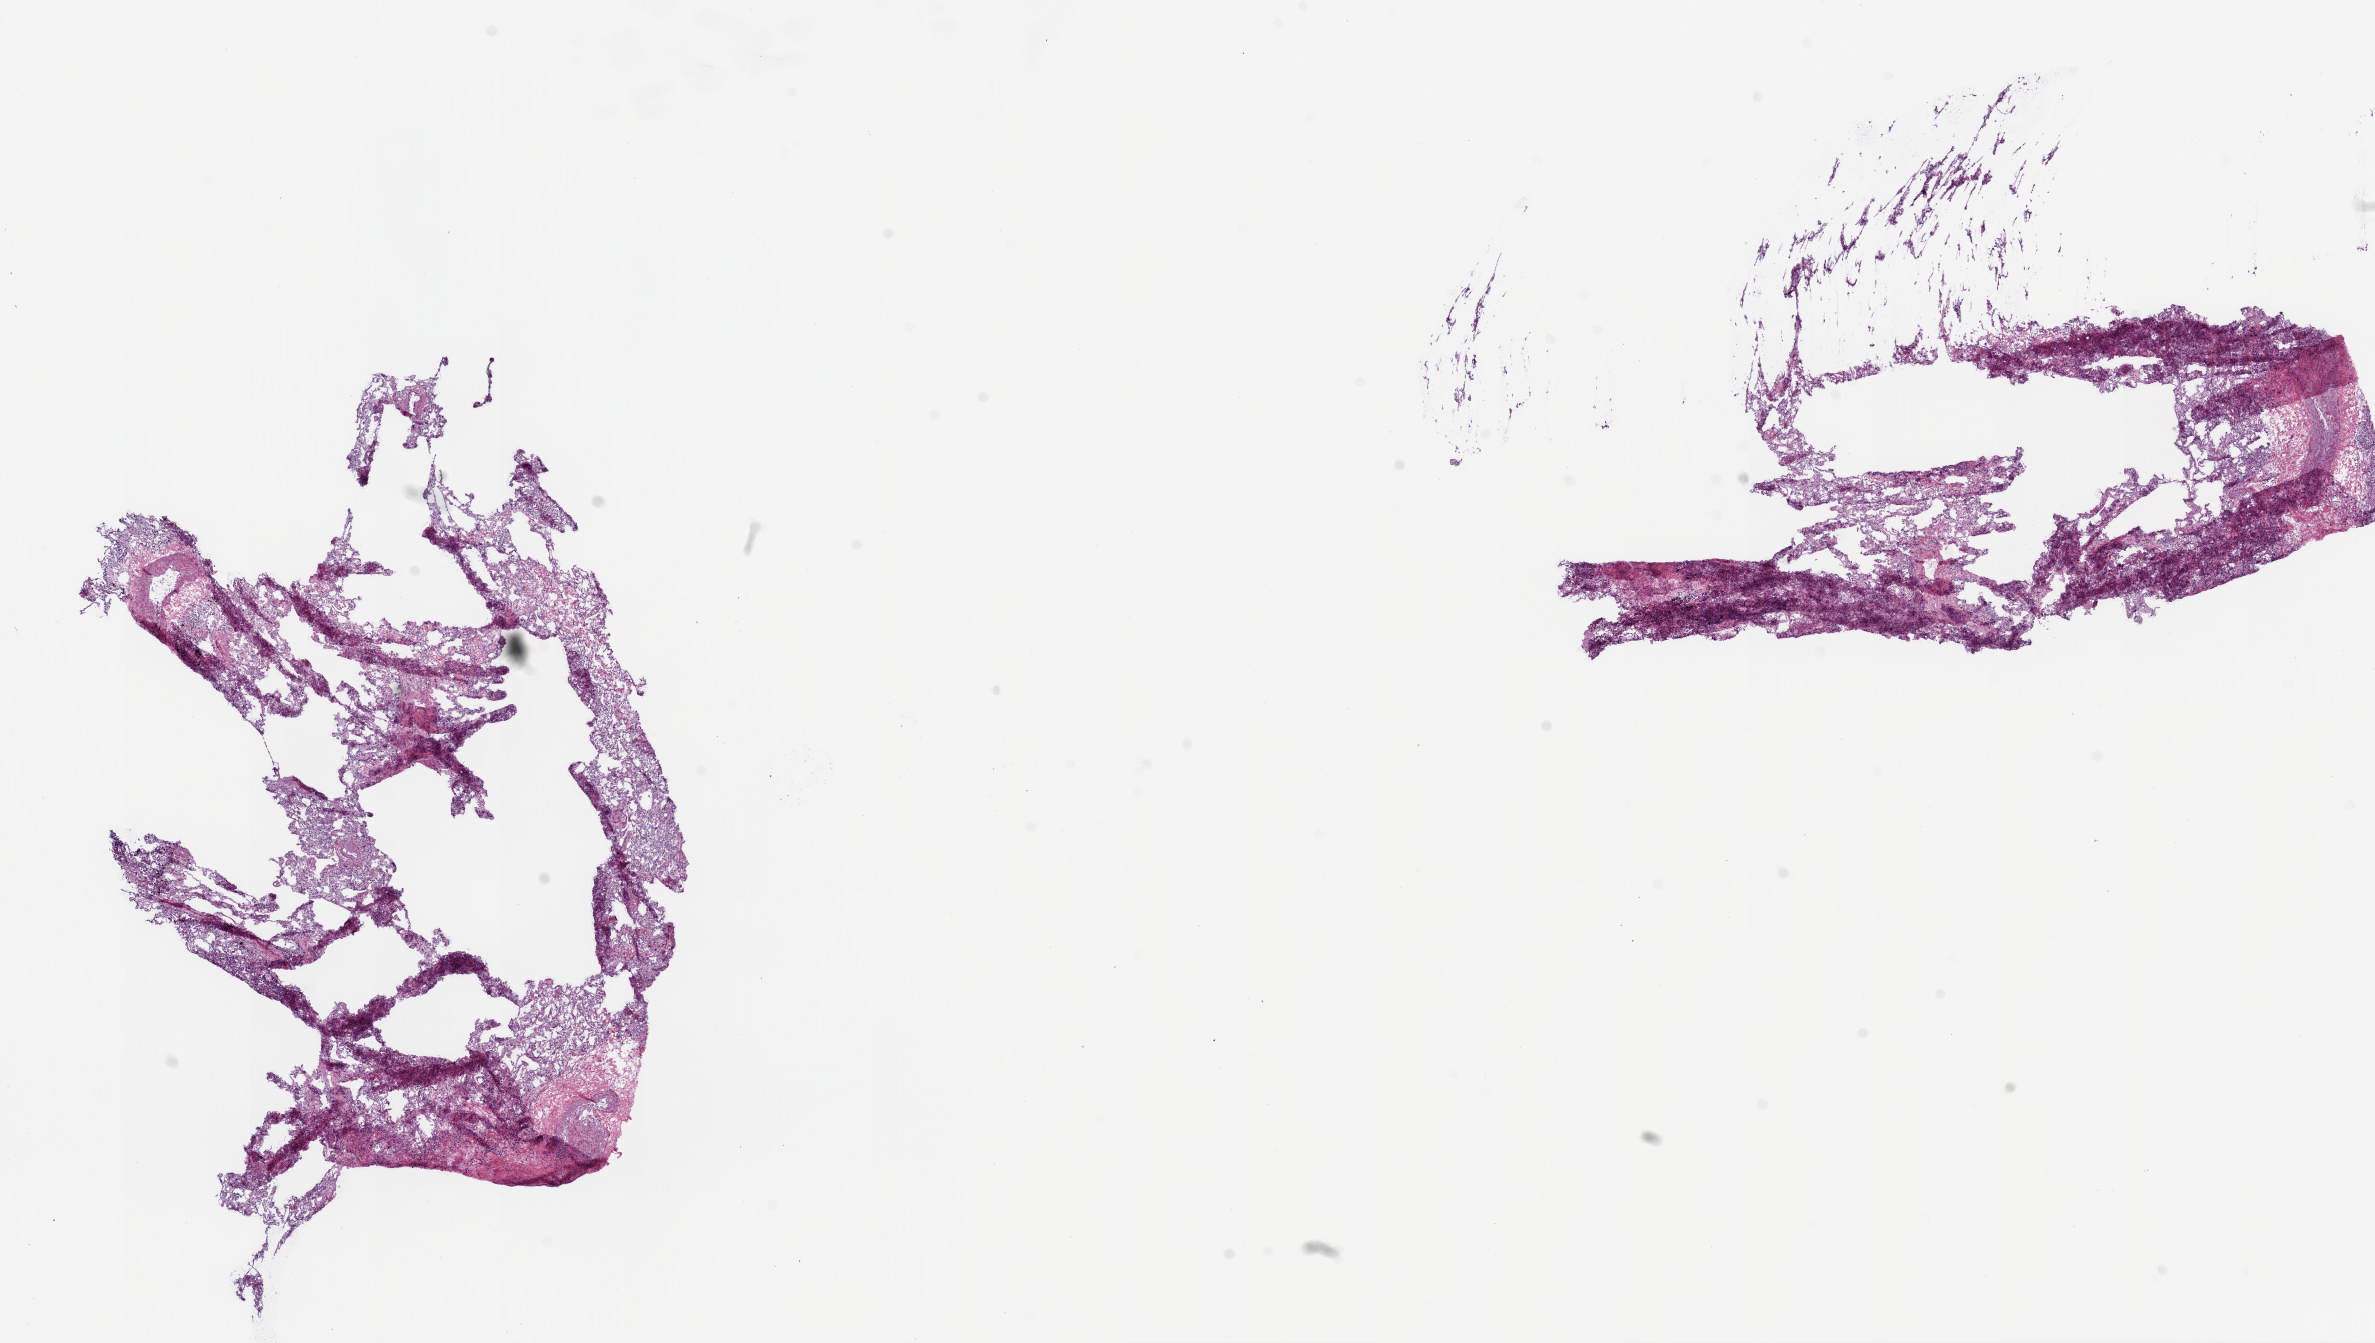
Digitized H&E-stained tissue section (whole slide), shown as a low-resolution overview of the whole scanned area (about 19.1 x 10.8 mm, from a 20x scan). Frozen section from the top of the tissue portion. Solid tissue normal (non-tumour tissue) sample from the lung. Male patient; age at initial diagnosis 67 years.
This section: solid tissue normal sample (biorepository sample class). Patient diagnosis: Adenocarcinoma, NOS.